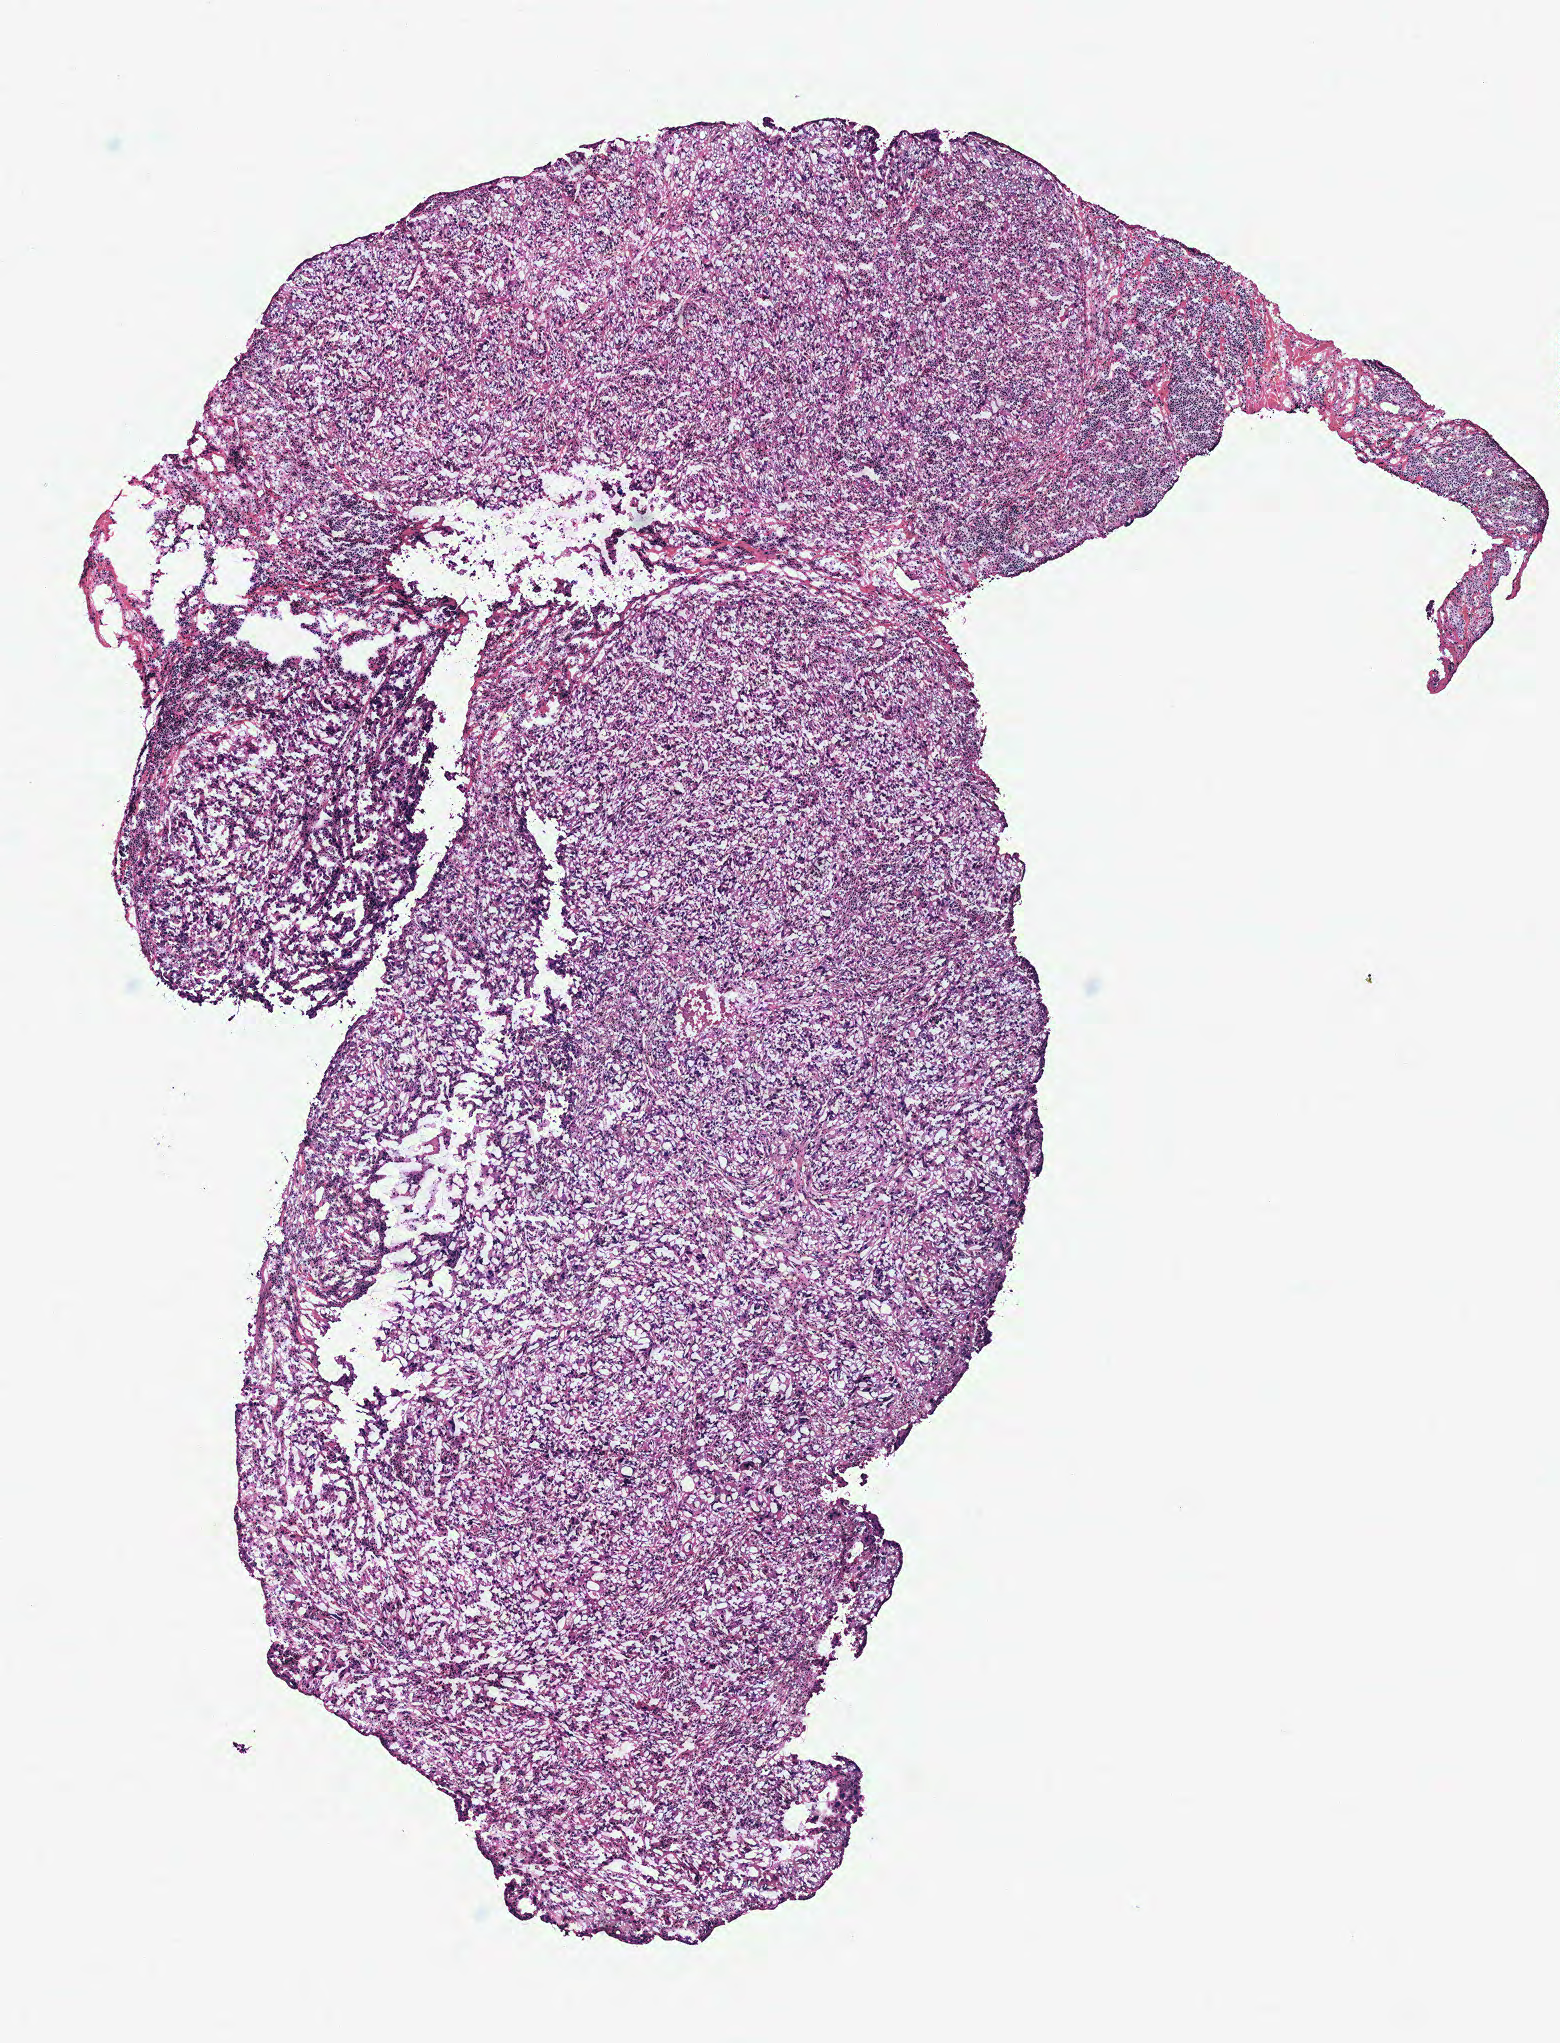
Digitized H&E tissue section (whole slide) — a low-resolution overview of the entire scanned area, about 6.2 x 8.2 mm. Breast, tissue type not recorded.
Patient diagnosis (cohort enrolment): breast cancer (breast).